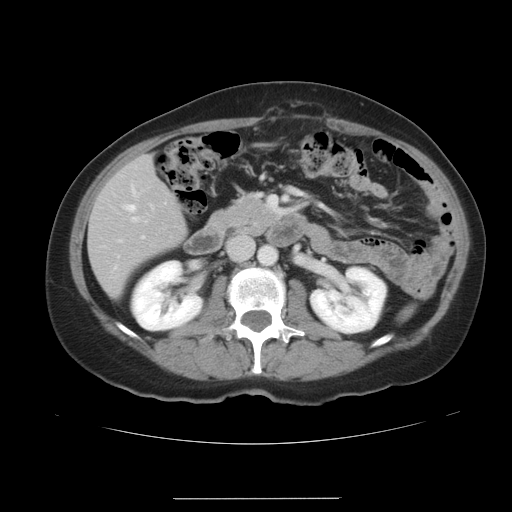
Contrast-enhanced abdominal CT, one axial slice; position 15 of 41 along the scan axis; 120 kVp; intravenous contrast given; soft-tissue window (W 400 / L 40 HU); 5 mm slice thickness; 512 × 512 image matrix, field of view 381 × 381 mm. Female patient, age 63 years. From the clinical record (not read from this slice): diagnosis: colorectal cancer liver metastases, imaged before liver resection; multiple liver metastases: yes; largest metastasis: 1.5 cm; disease in both lobes: yes.
Annotated regions visible in this slice (expert manual segmentation):
- hepatic veins: bounding box (x1, y1, x2, y2) in pixels: (126, 205, 135, 211)
- liver: (90, 157, 187, 296)
- planned liver remnant (the part of the liver to remain after resection): (90, 177, 187, 296)
- portal vein (with intrahepatic branches): (131, 217, 139, 222)